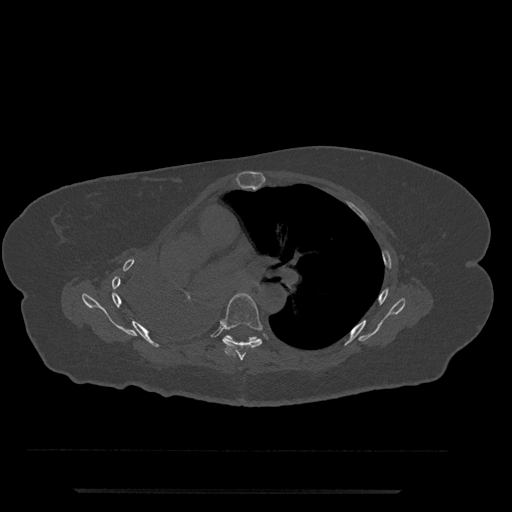
CT including the spine, one axial slice; slice 486 of 797 in the series (ordered by position); bone window (W 1800 / L 400 HU); 512 × 512 image matrix. Patient: female, 51 years. Case-level facts recorded for this patient, not image findings: primary cancer: neuro; vertebrae with lytic lesions (as recorded): T8.
Annotated regions visible in this slice (semi-automatic segmentation, software-assisted and operator-edited):
- T6 vertebra: box from (x=221, y=293) to (x=262, y=361) px
- T7 vertebra: (x=226, y=335)–(x=259, y=341)